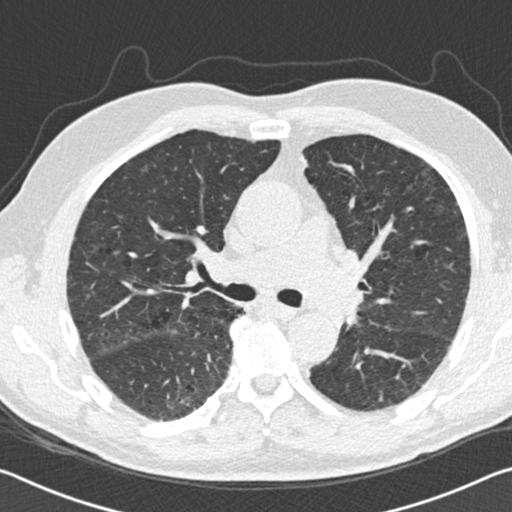
Low-dose screening chest CT, axial slice, second screening round (one year after baseline), lung window (W 1500 / L -600 HU), slice 60 of 142 in the series. Male, age 69 years at enrolment.
Lesion marked by an expert reader, box from (x=159, y=377) to (x=208, y=426) px. Reader record for this screening exam (exam-level; its link to the box is not recorded): non-calcified nodule or mass ≥4 mm, right lower lobe, 10 × 10 mm, spiculated (stellate) margins, soft tissue attenuation, pre-existing on the prior screen: yes; interval growth: yes. Official screen result: positive, other. Later outcome: lung cancer diagnosed 290 days after this screen — squamous cell carcinoma, NOS, right lower lobe, moderately differentiated (G2), stage IA (AJCC 6th edition), 25 mm at pathology.